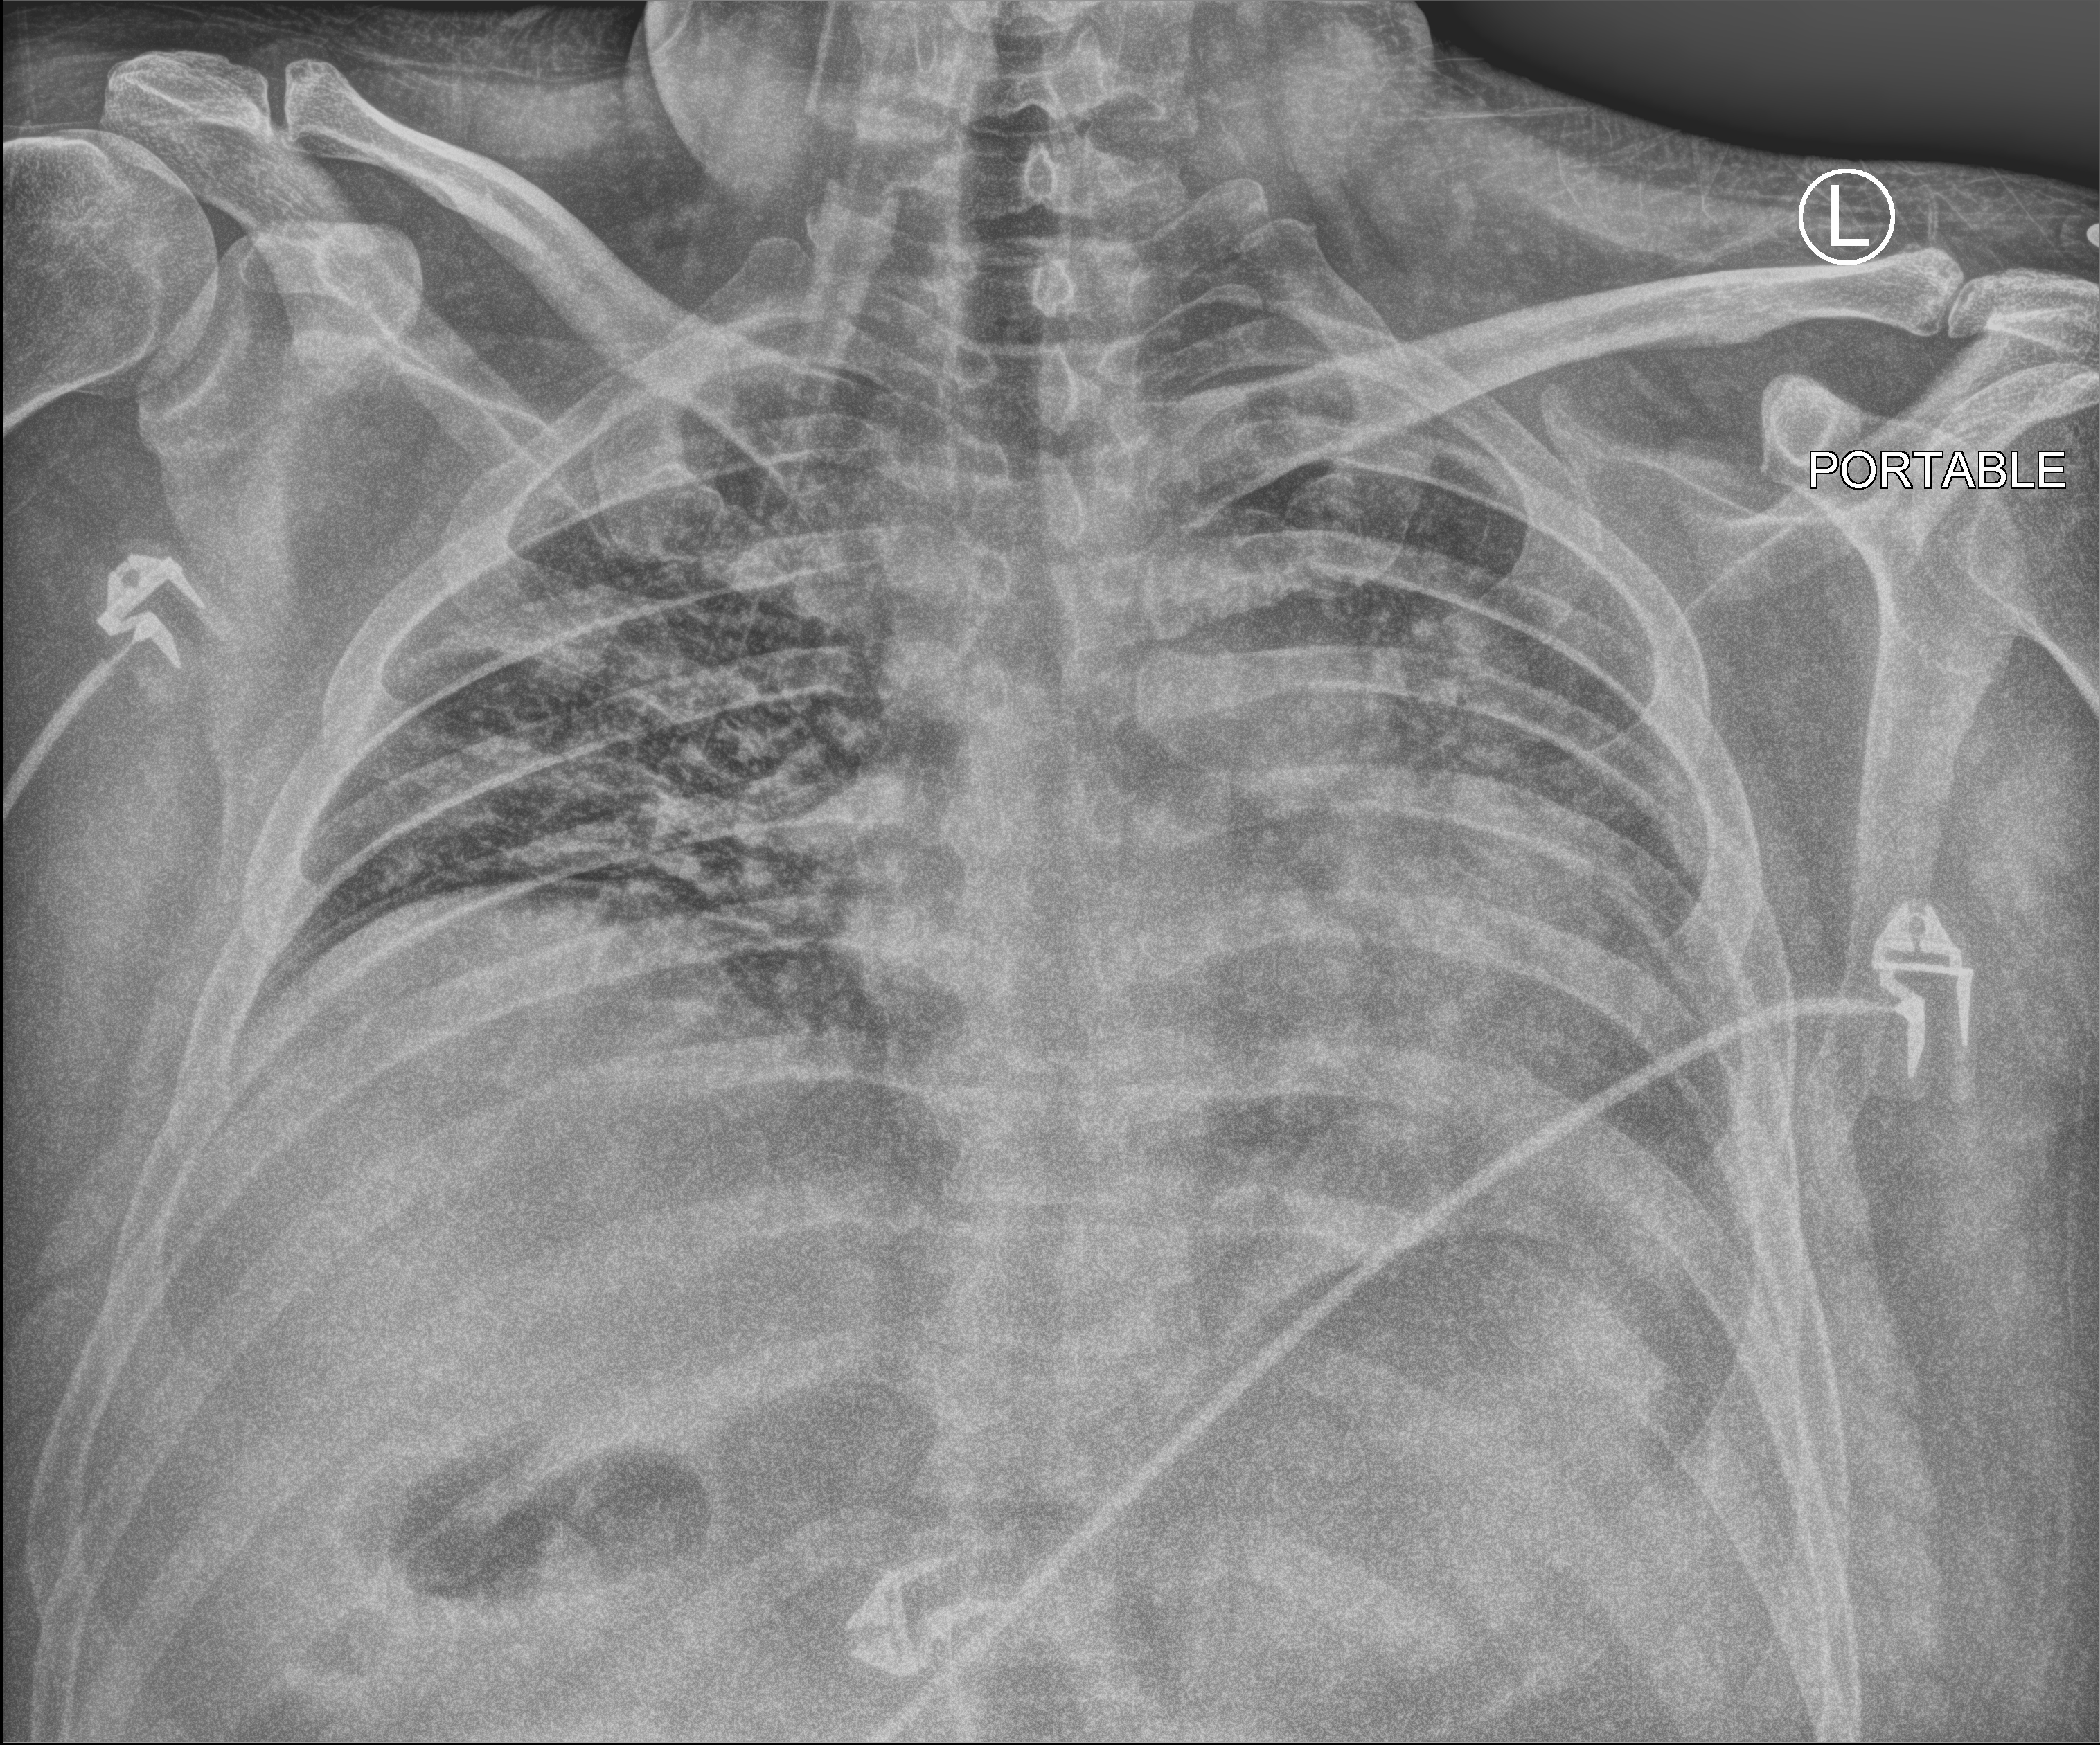
Chest X-ray (portable), anteroposterior (AP) projection. Patient hospitalised with COVID-19; male, aged 18–59 years.
Hospital-stay facts (about this admission, not read from this image; timing relative to this image not recorded): mechanically ventilated during this hospital stay: no.